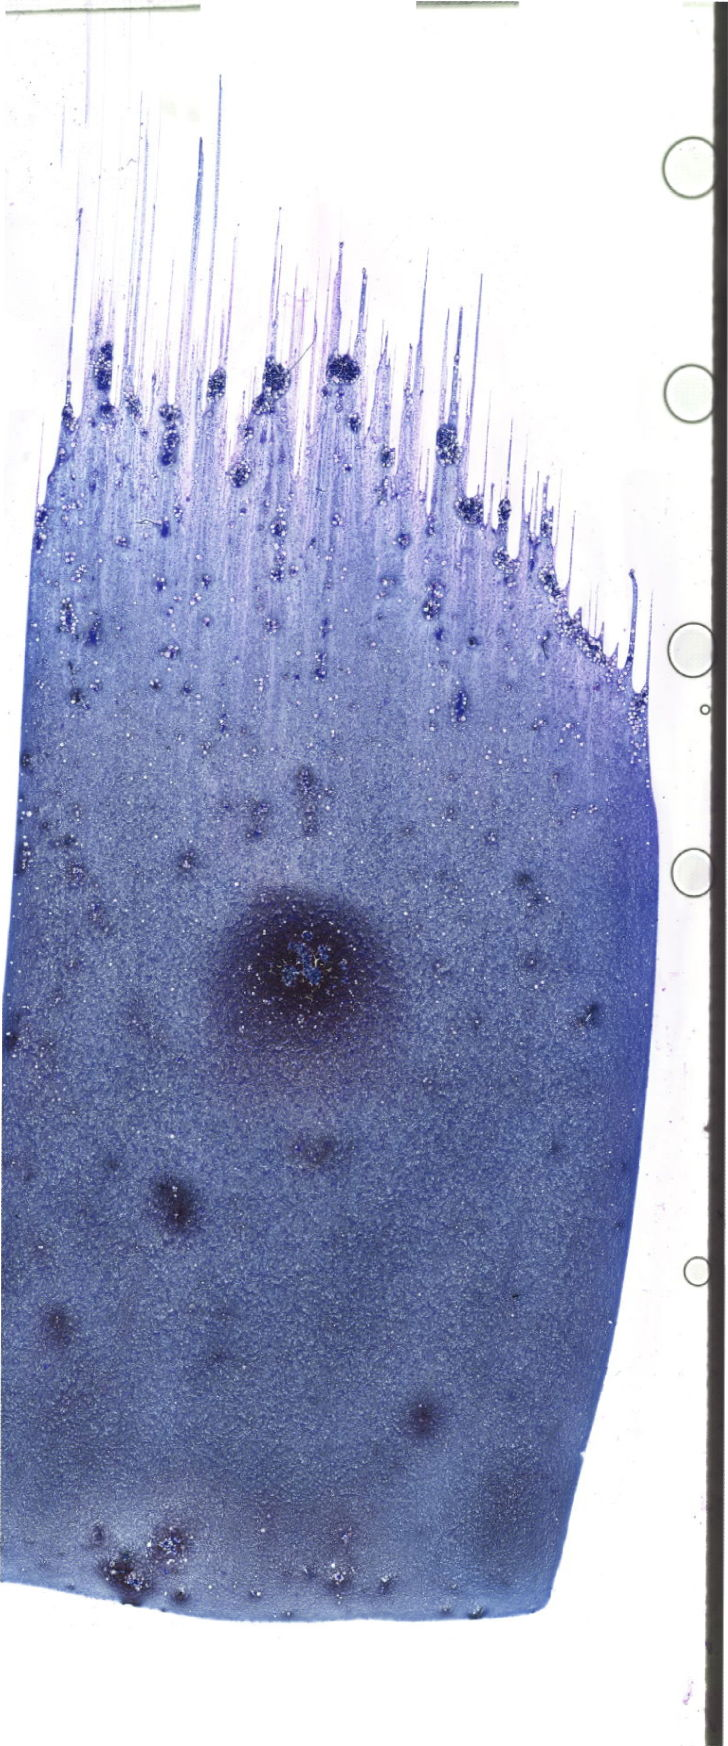
Bone marrow aspirate smear, May-Grünwald–Giemsa stain, whole-slide image, low-resolution overview of the scanned area, about 20.6 x 49.5 mm. Female patient.
• diagnosis: Acute Myeloid Leukemia without Maturation